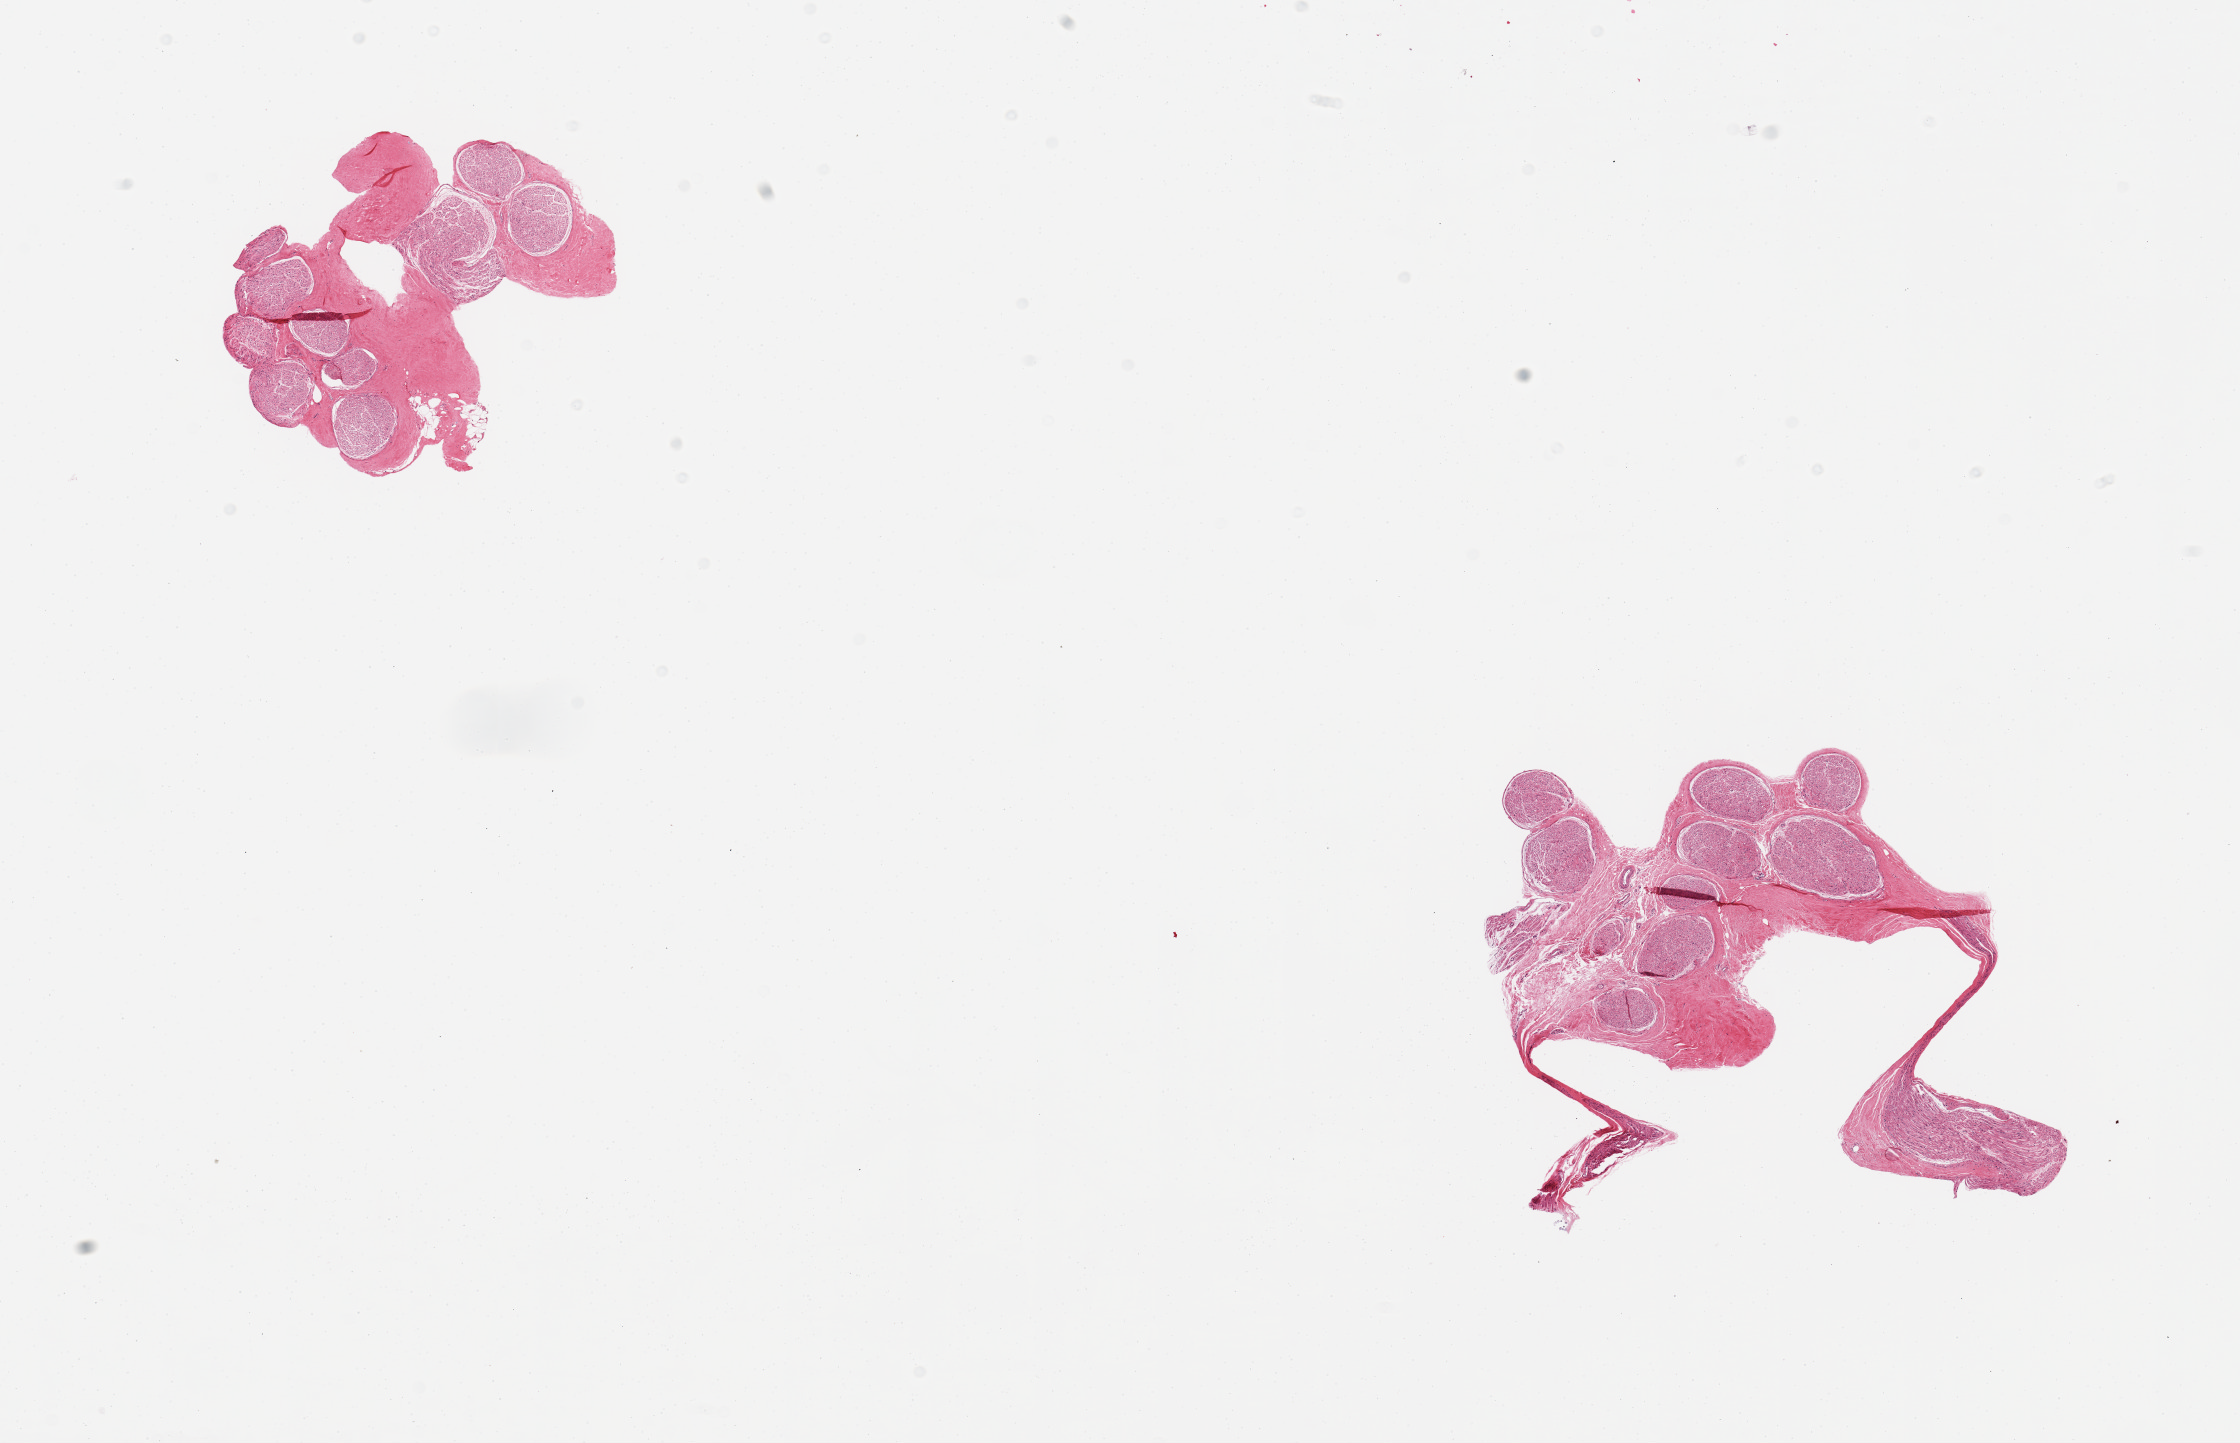
H&E whole-slide image, a low-resolution overview of the entire scanned area, about 17.7 x 11.4 mm (slide scanned at 20x); PAXgene-fixed, paraffin-embedded tissue; section of tibial nerve (target tissue); tissue donor sample. Donor: male.
Review note (as recorded): 2 pieces; 20% fibrous stroma; no adherent or internal fat.